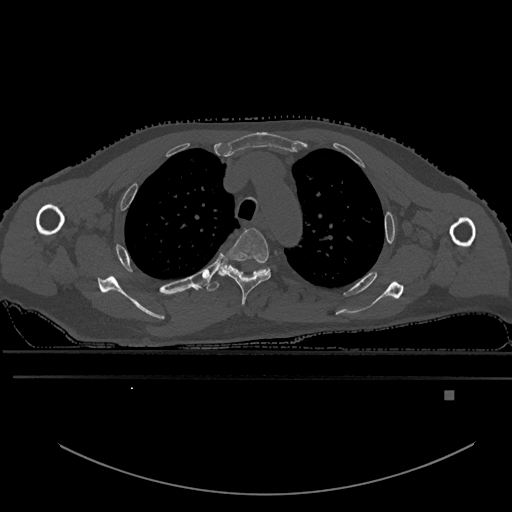
CT including the spine, one axial slice; position 440 of 969 along the scan axis; bone window (W 1800 / L 400 HU); 0.5 mm slice thickness; 512 × 512 image matrix, field of view 456 × 456 mm. Male patient, age 82 years. From the clinical record (not read from this slice): primary cancer: prostate.
Outlined on this slice (semi-automatically segmented with operator editing):
- T3 vertebra: box from (x=218, y=228) to (x=271, y=305) px
- T4 vertebra: (x=206, y=261)–(x=270, y=292)